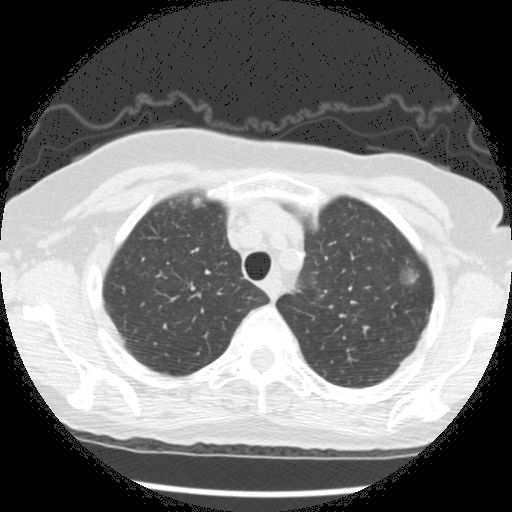
Low-dose screening chest CT, one axial slice. 120 kVp. Lung window (W 1500 / L -600 HU). 512 × 512 image matrix, field of view 320 × 320 mm.
Outlined on this slice (expert manual segmentation):
- lesion 1 (tumor, upper lobe of left lung): bounding box (x1, y1, x2, y2) in pixels: (410, 275, 415, 282)